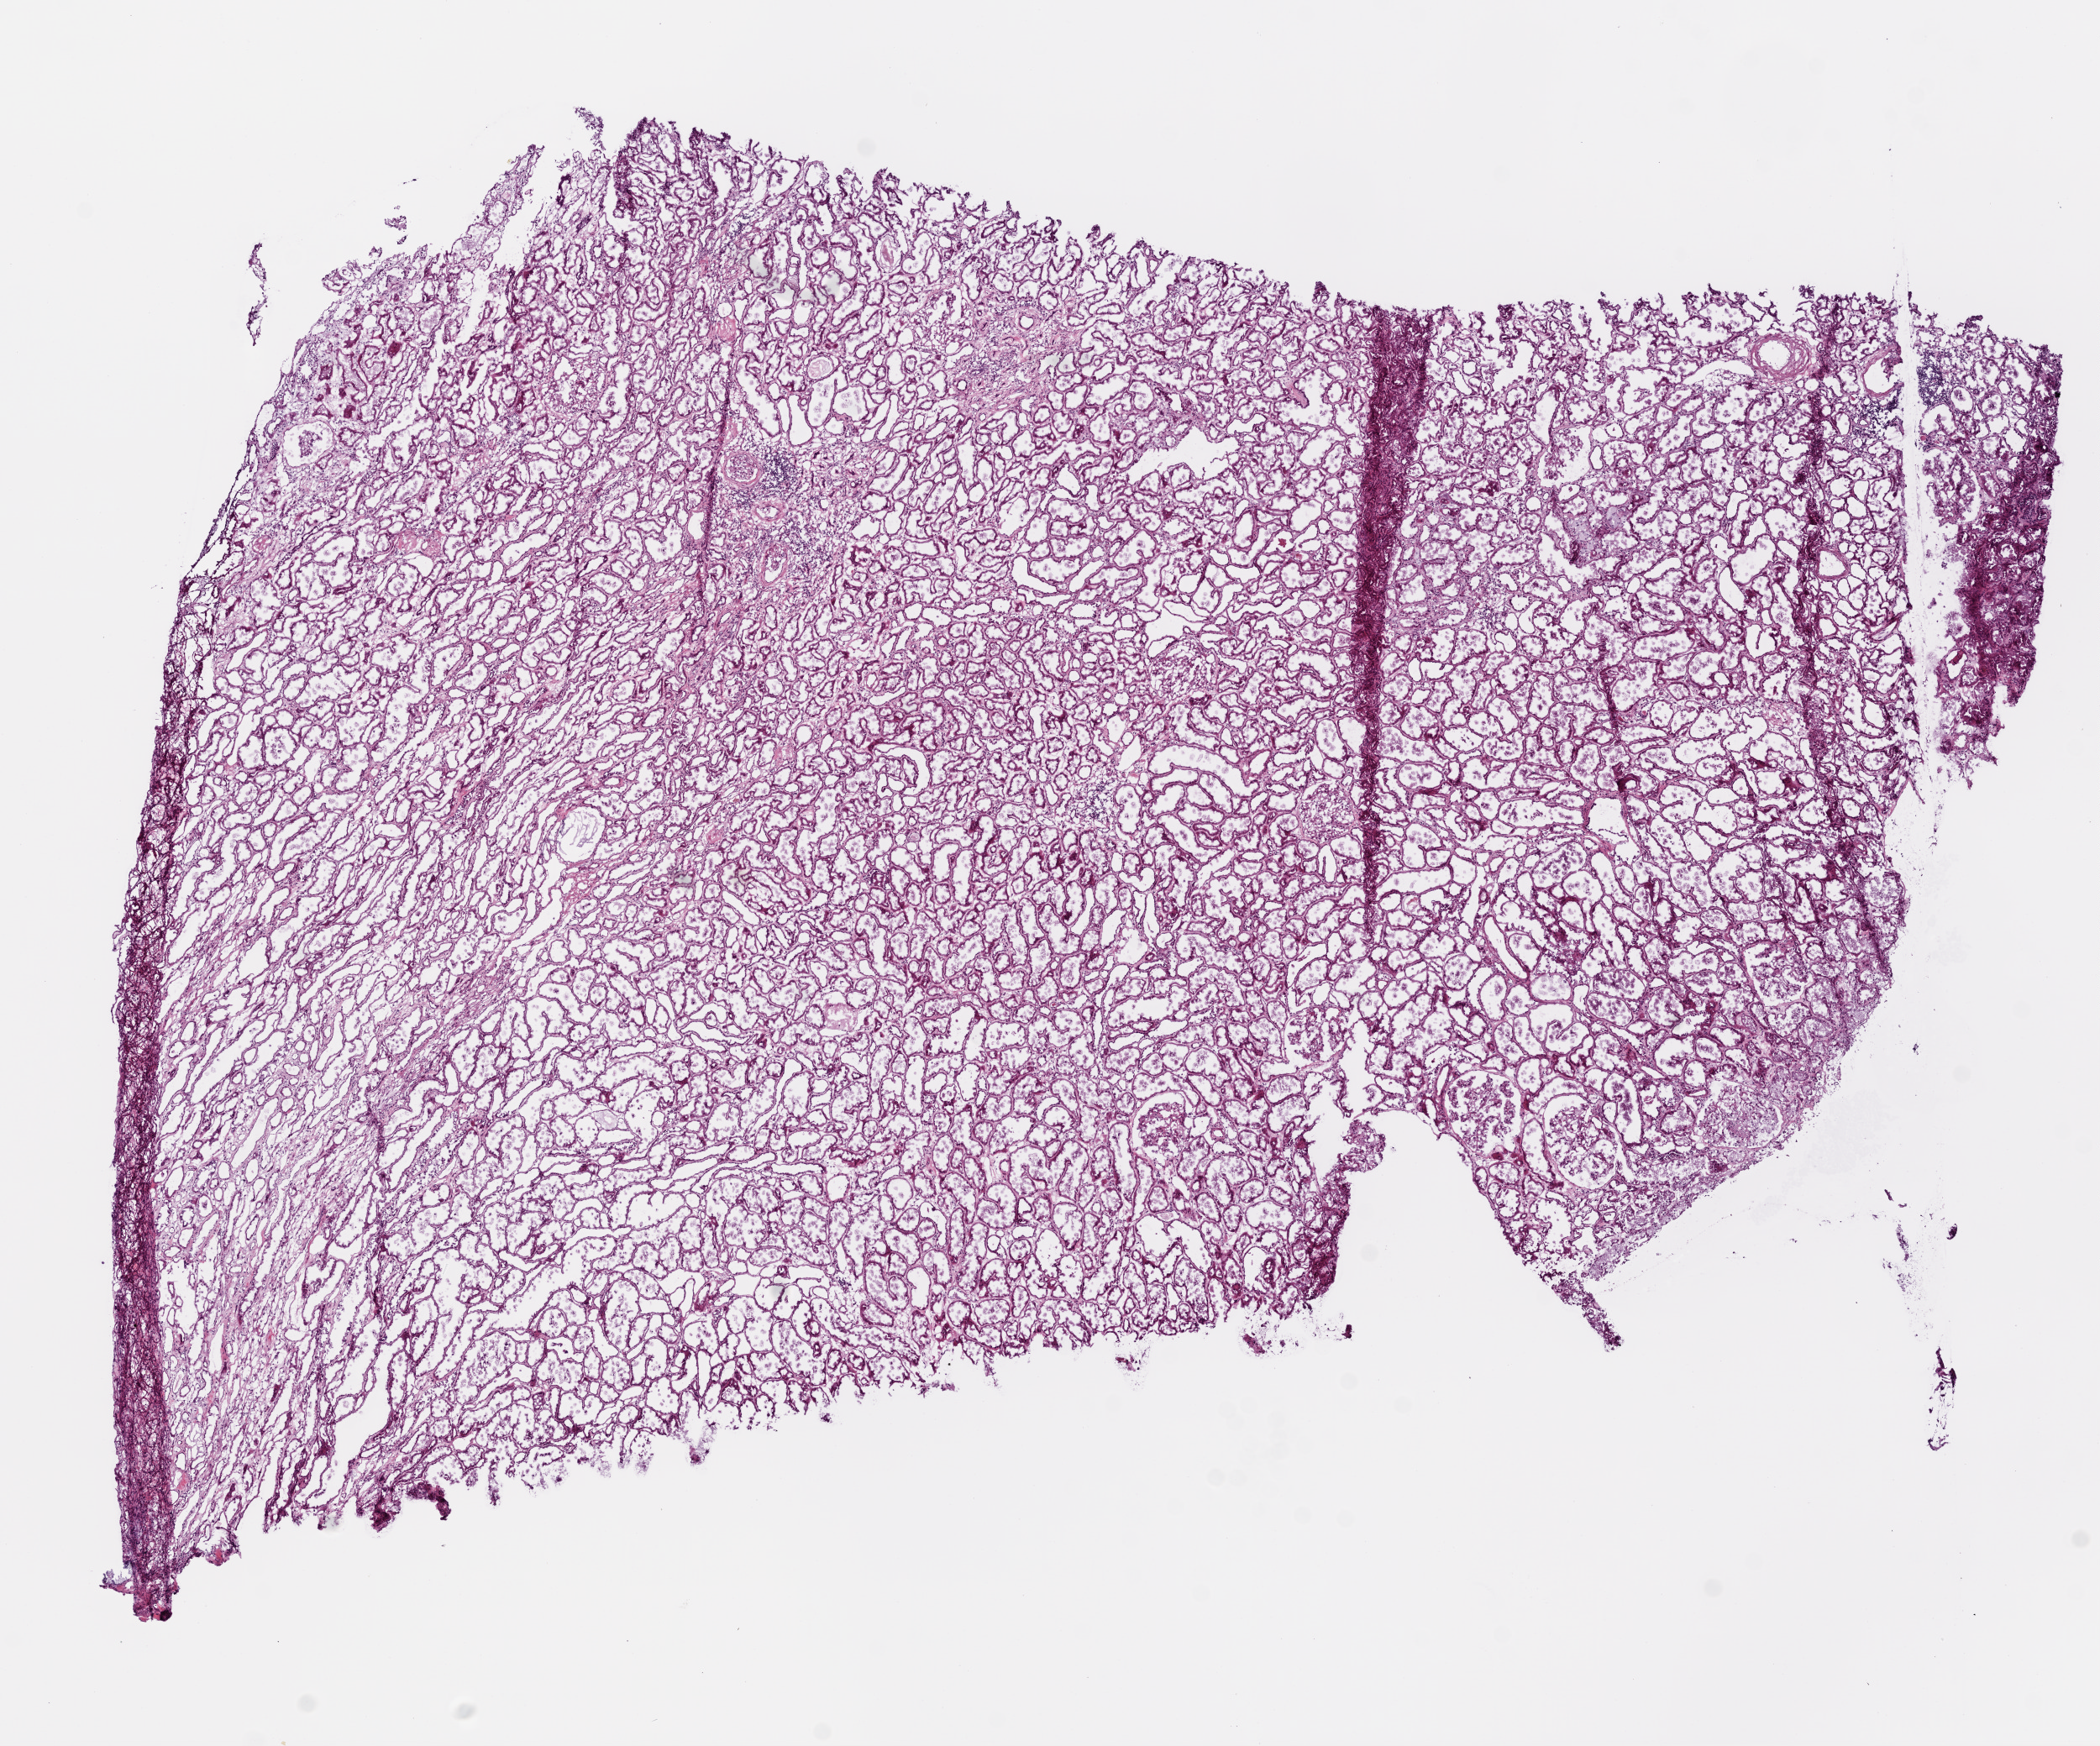
Whole-slide histology image, H&E-stained — shown as a low-resolution overview of the whole scanned area (about 10.0 x 8.3 mm), frozen section from the top of the tissue portion, kidney, solid tissue normal (non-tumour tissue) sample. Female, age 51 years at initial diagnosis.
This section: solid tissue normal sample (biorepository sample class). Patient diagnosis: Clear cell adenocarcinoma, NOS.